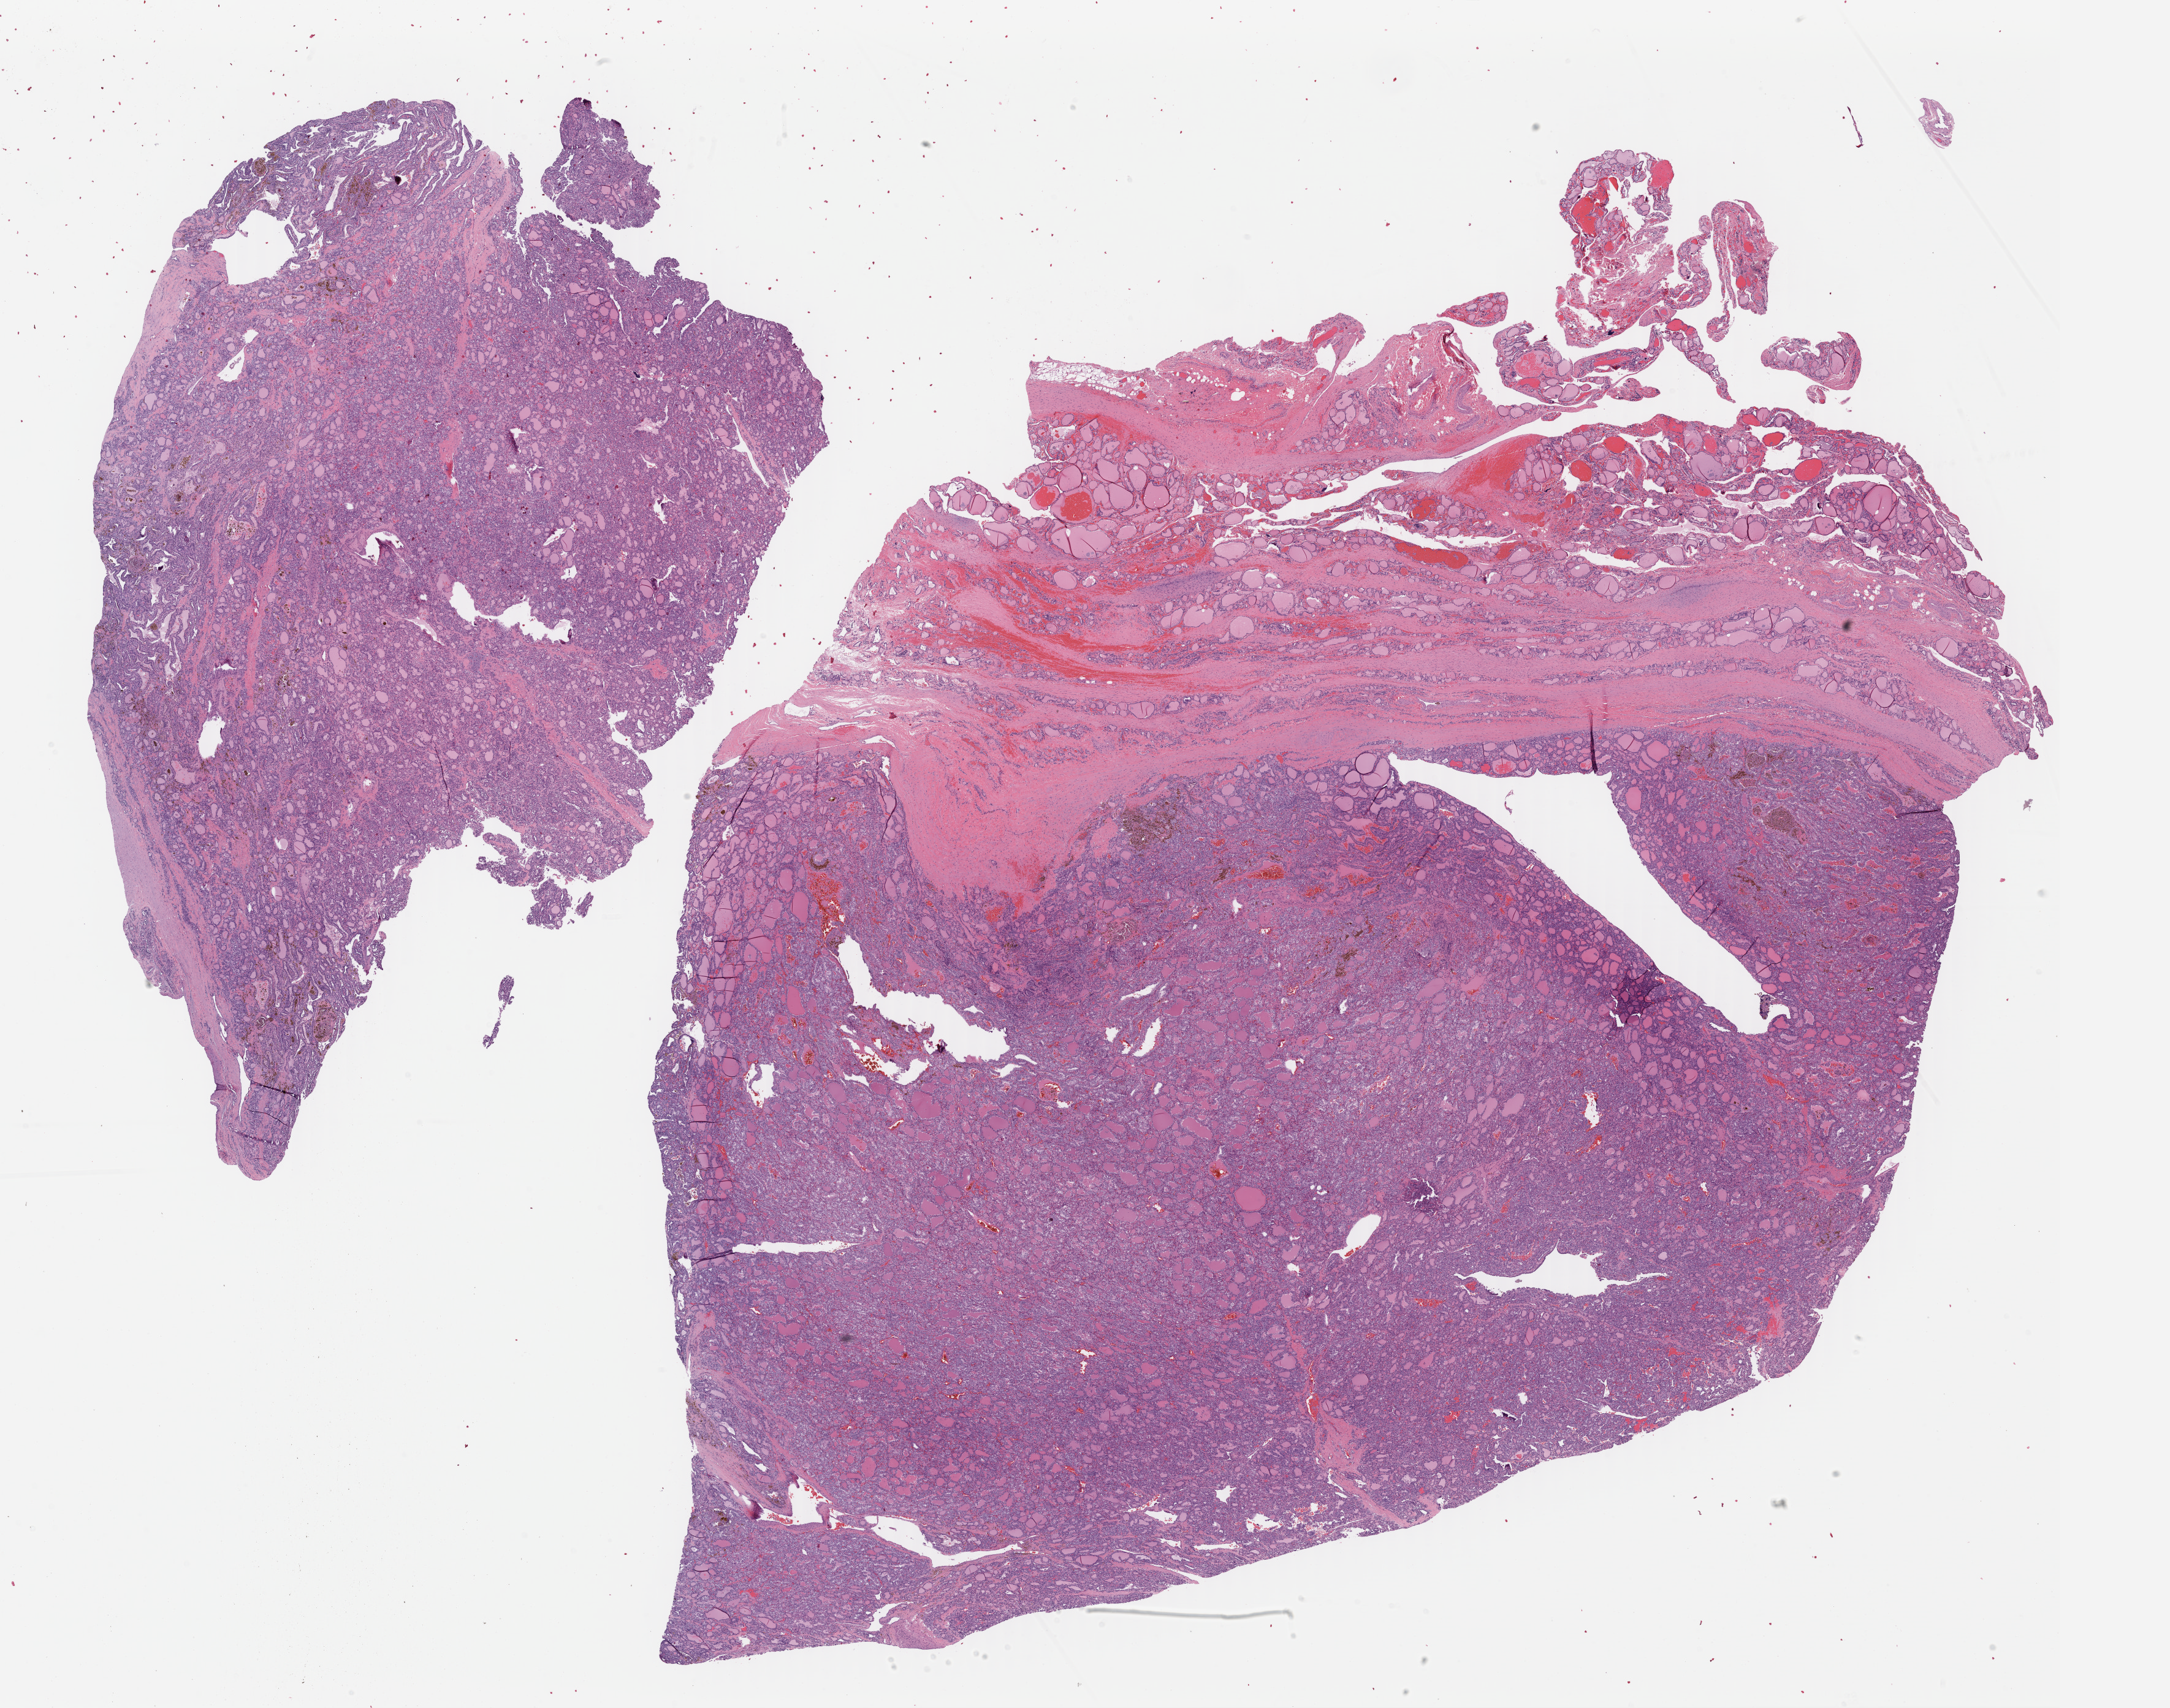
Digitized H&E-stained tissue section (whole slide), low-resolution overview of the scanned area, about 27.8 x 21.9 mm; formalin-fixed paraffin-embedded (FFPE) diagnostic section; sample: primary tumour, thyroid. Patient: male, age at initial diagnosis 41 years.
Histologic diagnosis: Papillary adenocarcinoma, NOS (thyroid gland). Lymph nodes positive (case pathology): 4 of 18 examined. AJCC pathologic stage: I (7th edition).